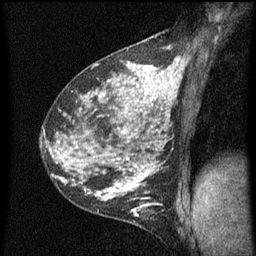
Breast MRI (dynamic contrast-enhanced), one sagittal slice; slice 35 of 60 in the series (ordered by position); dynamic contrast-enhanced series, image 2 of 5 at this slice position (ordered by acquisition); 1.5 T; TE 4.2 ms, TR 8 ms; 256 × 256 image matrix, field of view 180 × 180 mm. Patient: female, 35 years.
Structures marked on this image (semi-automatic segmentation, software-assisted and operator-edited):
- analysis volume of interest (the breast-tissue region the enhancement analysis was run in; not a lesion): box from (x=118, y=190) to (x=162, y=229) px
- tumour enhancement mask (voxels above the 70 % enhancement threshold inside the analysis volume of interest): (x=118, y=190)–(x=160, y=215)